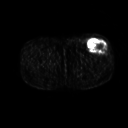
FDG PET of an extremity soft-tissue mass (from a PET/CT study), one axial slice; 128 × 128 image matrix, field of view 500 × 500 mm. Patient: male, 64 years. From the clinical record (not read from this slice): histological type: extraskeletal osteosarcoma; grade: high; site of the primary tumour: thigh.
Outlined on this slice (expert contour drawn on MRI and transferred to this co-registered scan by the dataset authors):
- gross tumour volume (mass): box from (x=87, y=39) to (x=107, y=53) px